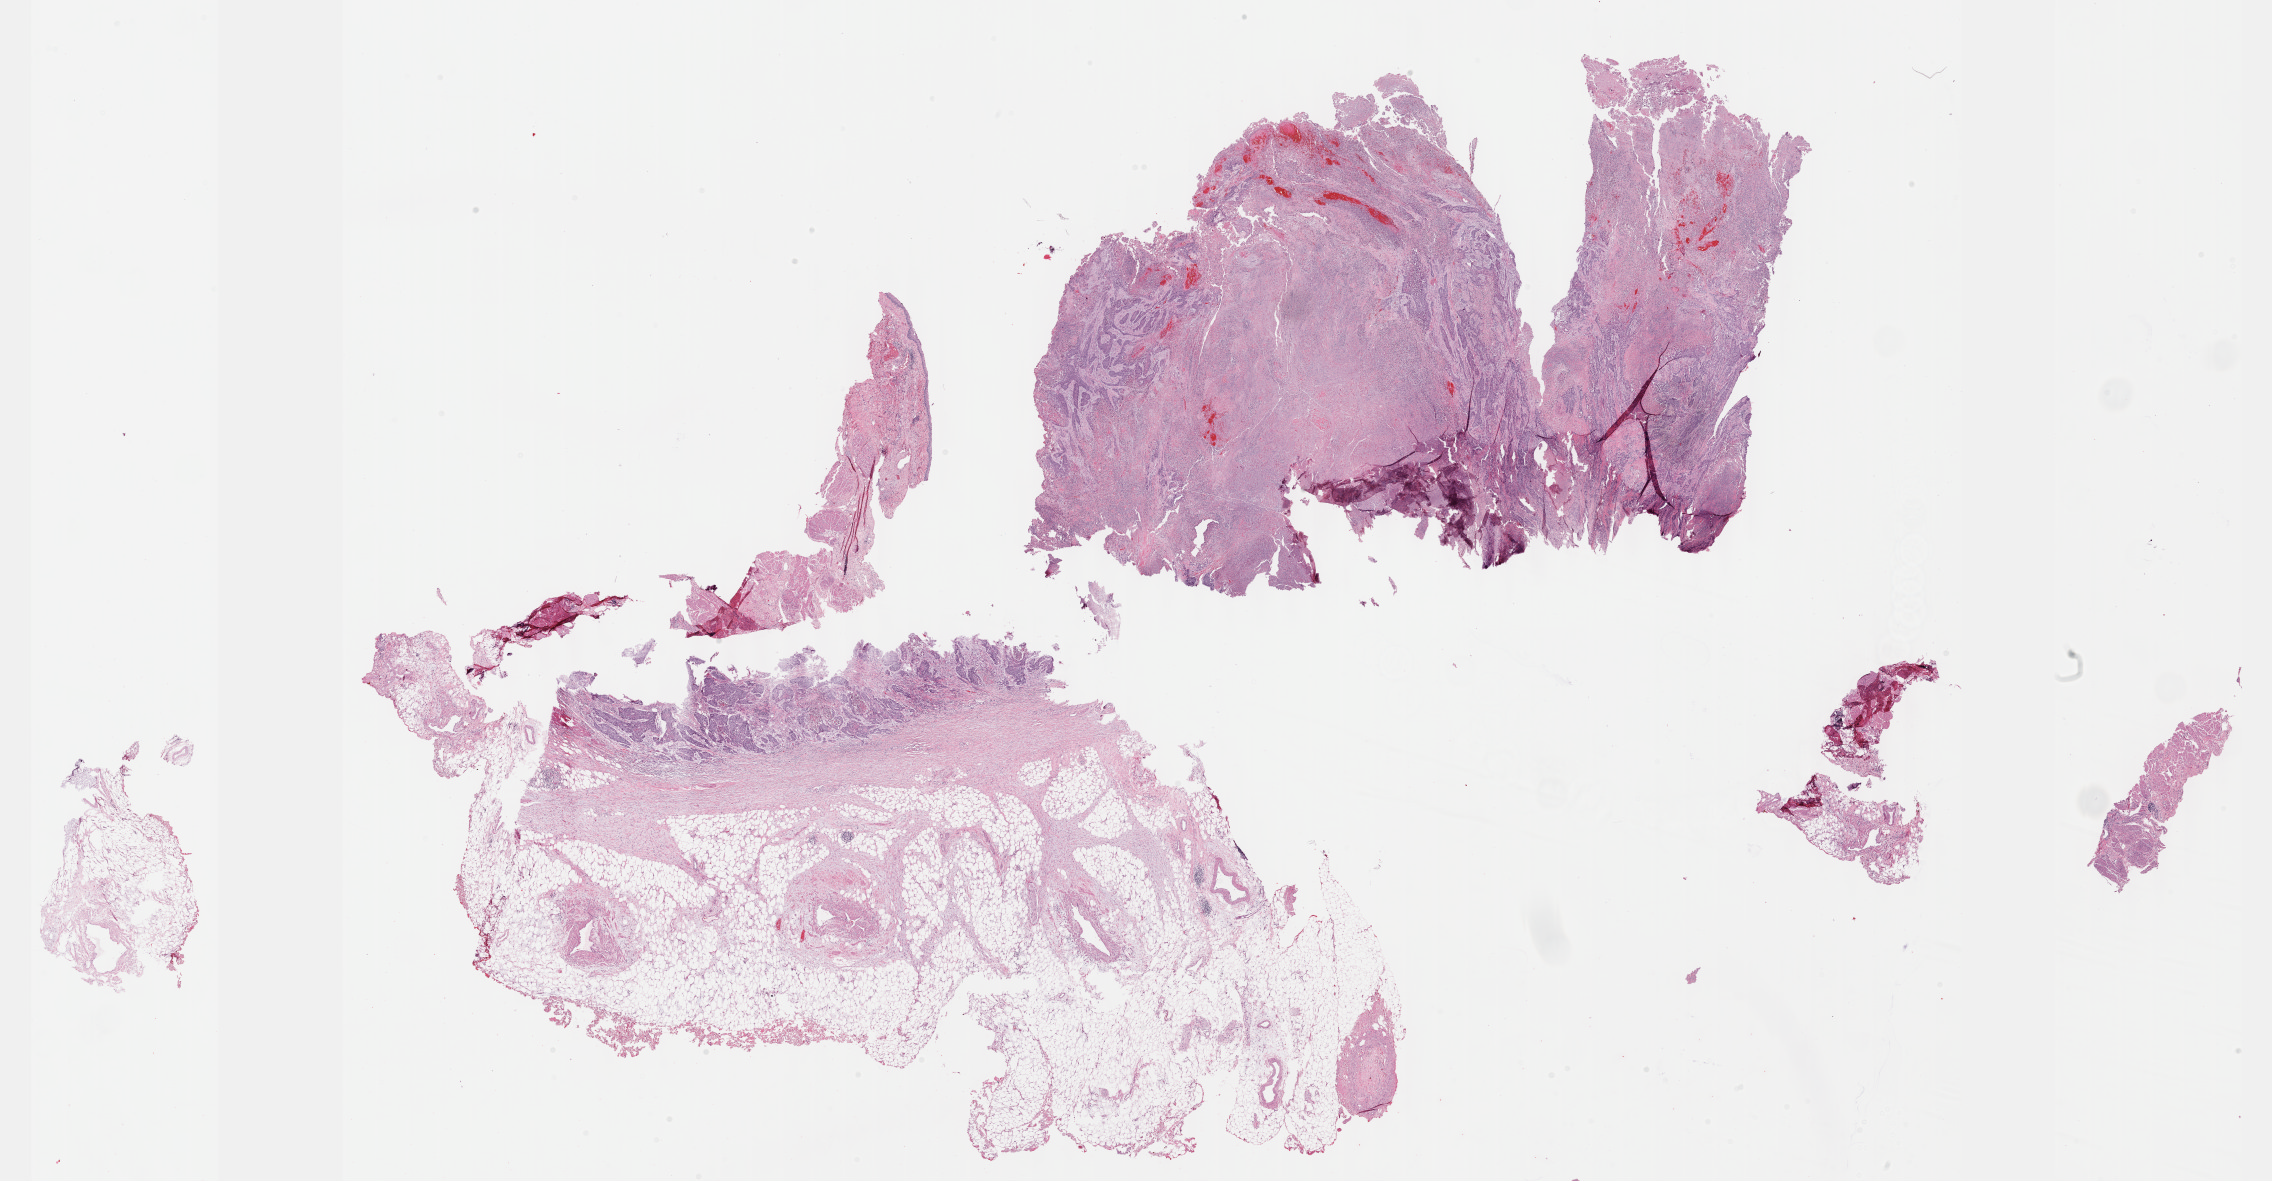
Whole-slide histology image, H&E-stained, a low-resolution overview of the entire scanned area, about 36.7 x 19.1 mm (from a 40x scan), FFPE section, bladder, primary tumour sample. Patient: male, age at initial diagnosis 67 years. Histologic grade: high grade.
* lymph nodes positive (case pathology): 0 of 68 examined
* pathologic diagnosis: Transitional cell carcinoma
* AJCC pathologic stage: III (7th edition)